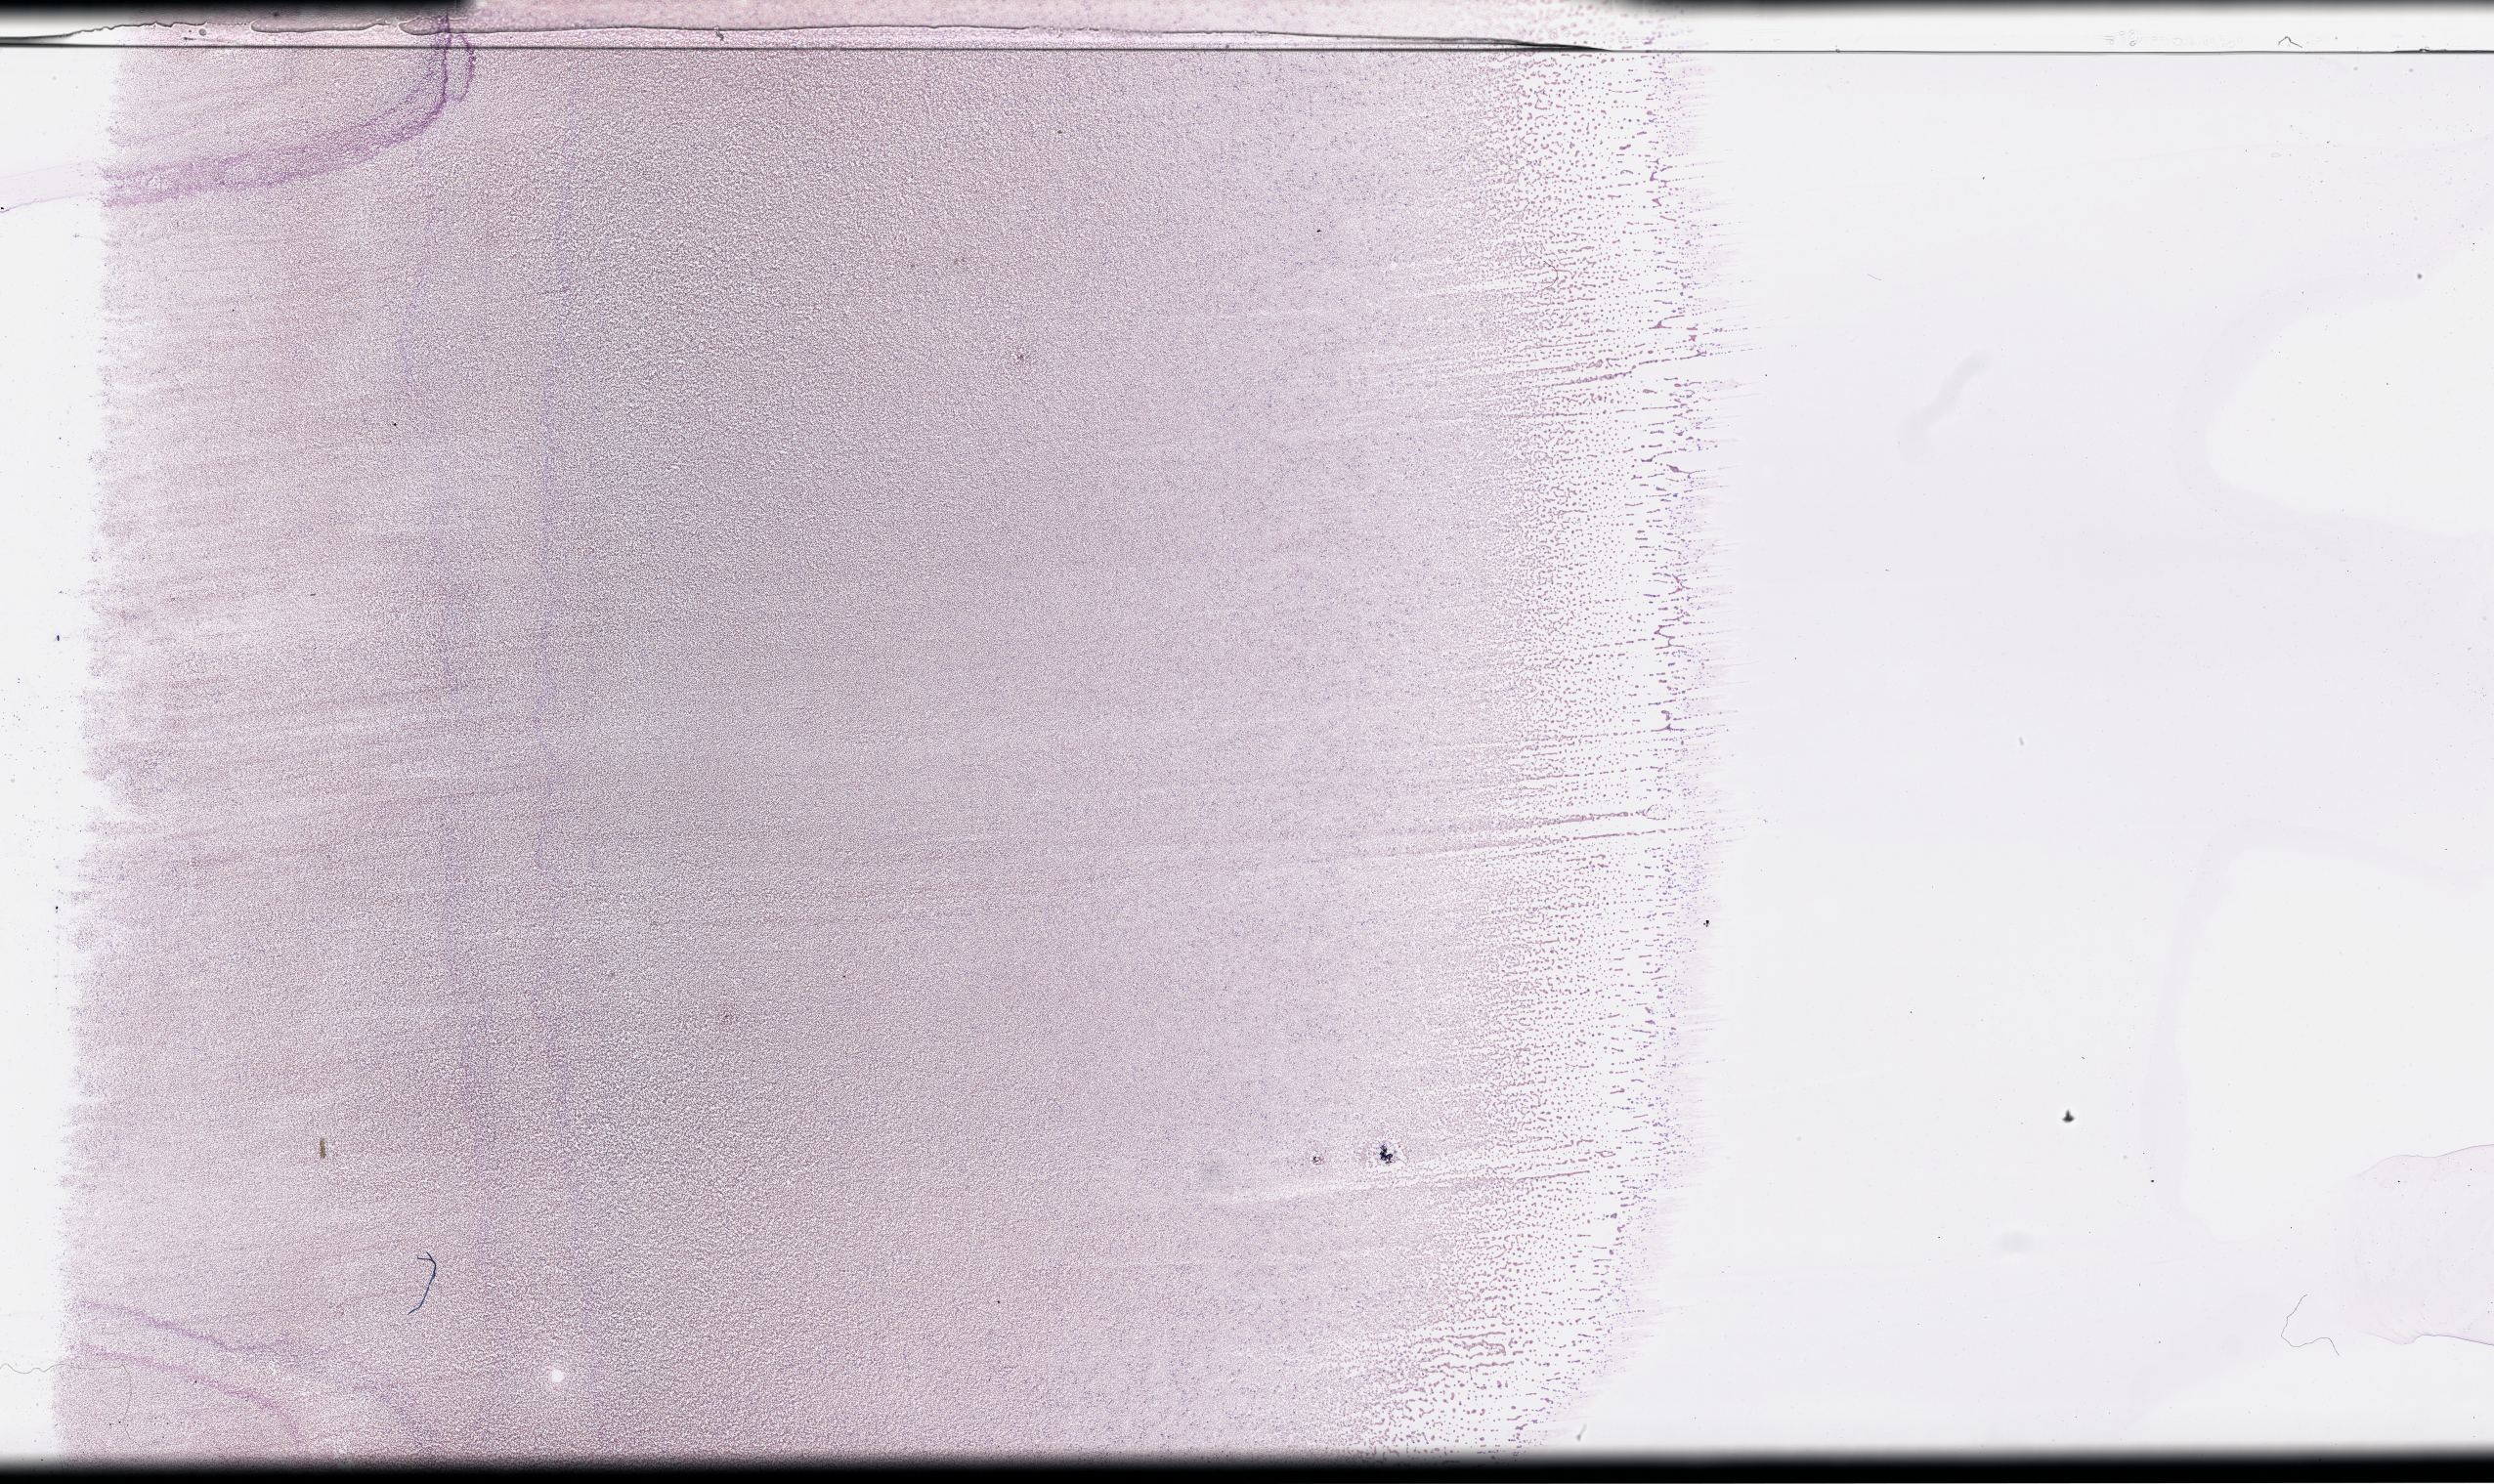
Whole-slide histology image, H&E-stained, shown as a low-resolution overview of the whole scanned area (about 41.2 x 24.5 mm, slide scanned at 40x), peripheral blood (leukaemic) sample. Patient: male, age 67 years.
* WHO classification: AML with maturation
* diagnosis: Acute Myeloid Leukemia
* FAB classification: M2